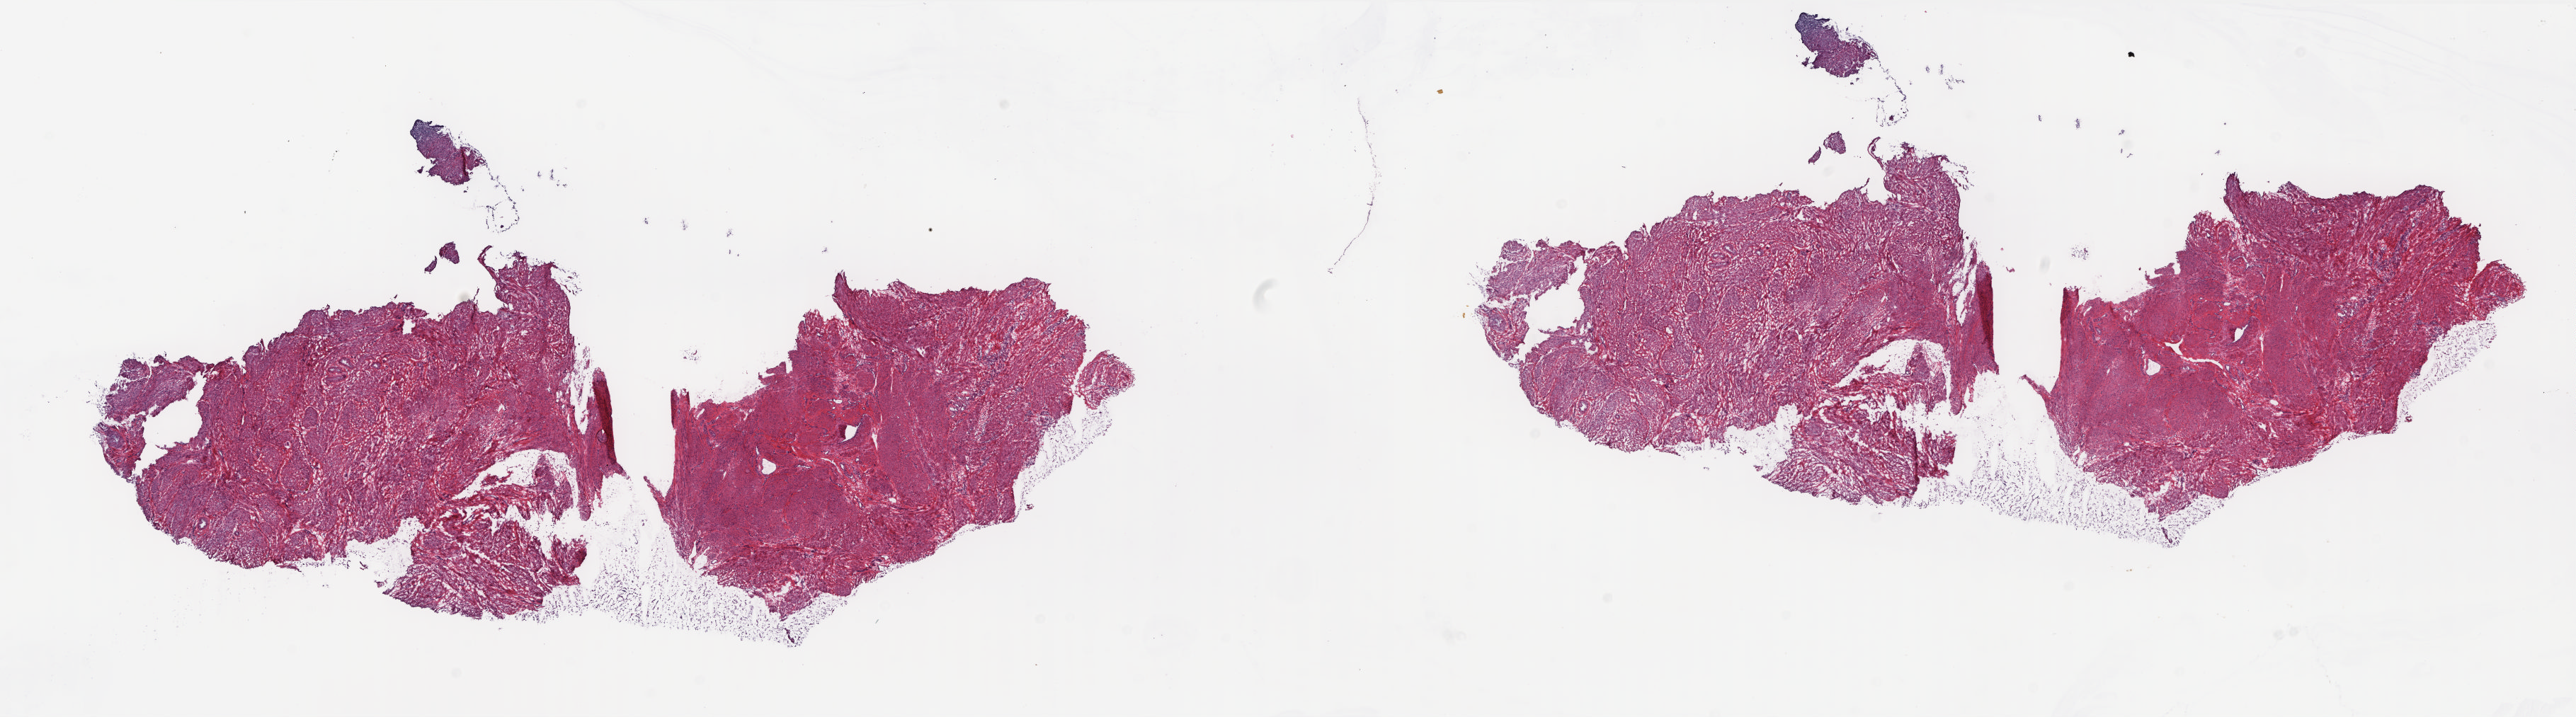
Digitized H&E-stained tissue section (whole slide), whole scanned area (about 29.3 x 8.2 mm) shown as a low-resolution overview; frozen section; solid tissue normal (non-tumour tissue) sample from the cervix. Female, age 51 years at initial diagnosis. Slide review estimates, as recorded: tumour cells 0%, tumour nuclei 0%, normal cells 100%, stromal cells 0%, necrosis 0%. Infiltration values recorded for this section: lymphocyte infiltration 1%, monocyte infiltration 0%, neutrophil infiltration 0%.
This section: solid tissue normal sample (biorepository sample class). Patient diagnosis: Squamous cell carcinoma, NOS (cervix uteri).